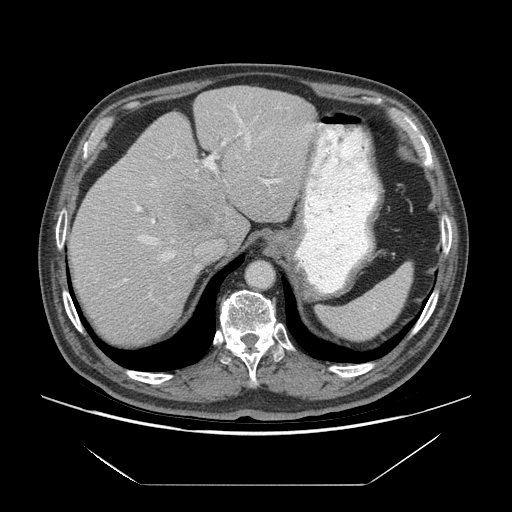
Contrast-enhanced abdominal CT (liver protocol), one axial slice; slice 51 of 75 in the series (ordered by position); 140 kVp; soft-tissue window (W 400 / L 40 HU); 2.5 mm slice thickness; 512 × 512 image matrix, field of view 420 × 420 mm. From the clinical record (not read from this slice): diagnosis: hepatocellular carcinoma (patient treated with transarterial chemoembolisation; whether this scan precedes or follows treatment is not stated here); TNM stage (as recorded): Stage-I.
Structures marked on this image (semi-automatically segmented with operator editing):
- liver parenchyma outside the tumour (the mass and vessels are separate outlines, so this box may not span the whole liver): bounding box (x1, y1, x2, y2) in pixels: (68, 86, 316, 344)
- mass: (159, 168, 228, 233)
- liver vessels: (124, 105, 311, 295)